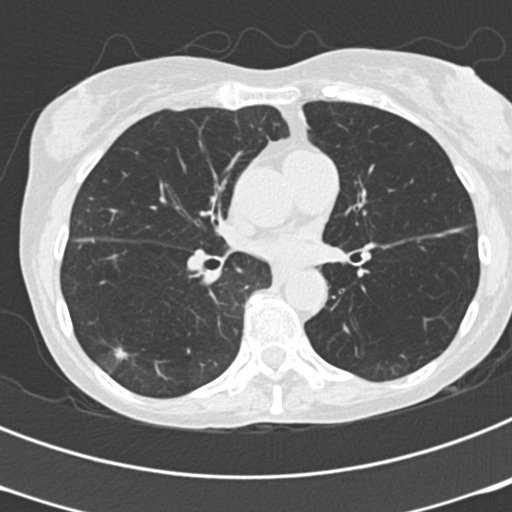
Axial slice from a low-dose chest CT screening exam, third annual screen, lung window (W 1500 / L -600 HU), 2 mm slice thickness. Female participant, aged 68 years at enrolment. Former smoker at enrolment.
Lesion marked by an expert reader, bounding box <102,335,140,366> (left, top, right, bottom; pixels). The exam's reader record, not a measurement of the box and not confirmed to be the same lesion: non-calcified nodule or mass ≥4 mm, right lower lobe, 9 × 5 mm, poorly defined margins, soft tissue attenuation, pre-existing on the prior screen: yes; interval growth: no. Official screen result: positive, no significant change: stable abnormalities potentially related to lung cancer, unchanged since the prior screening exam.